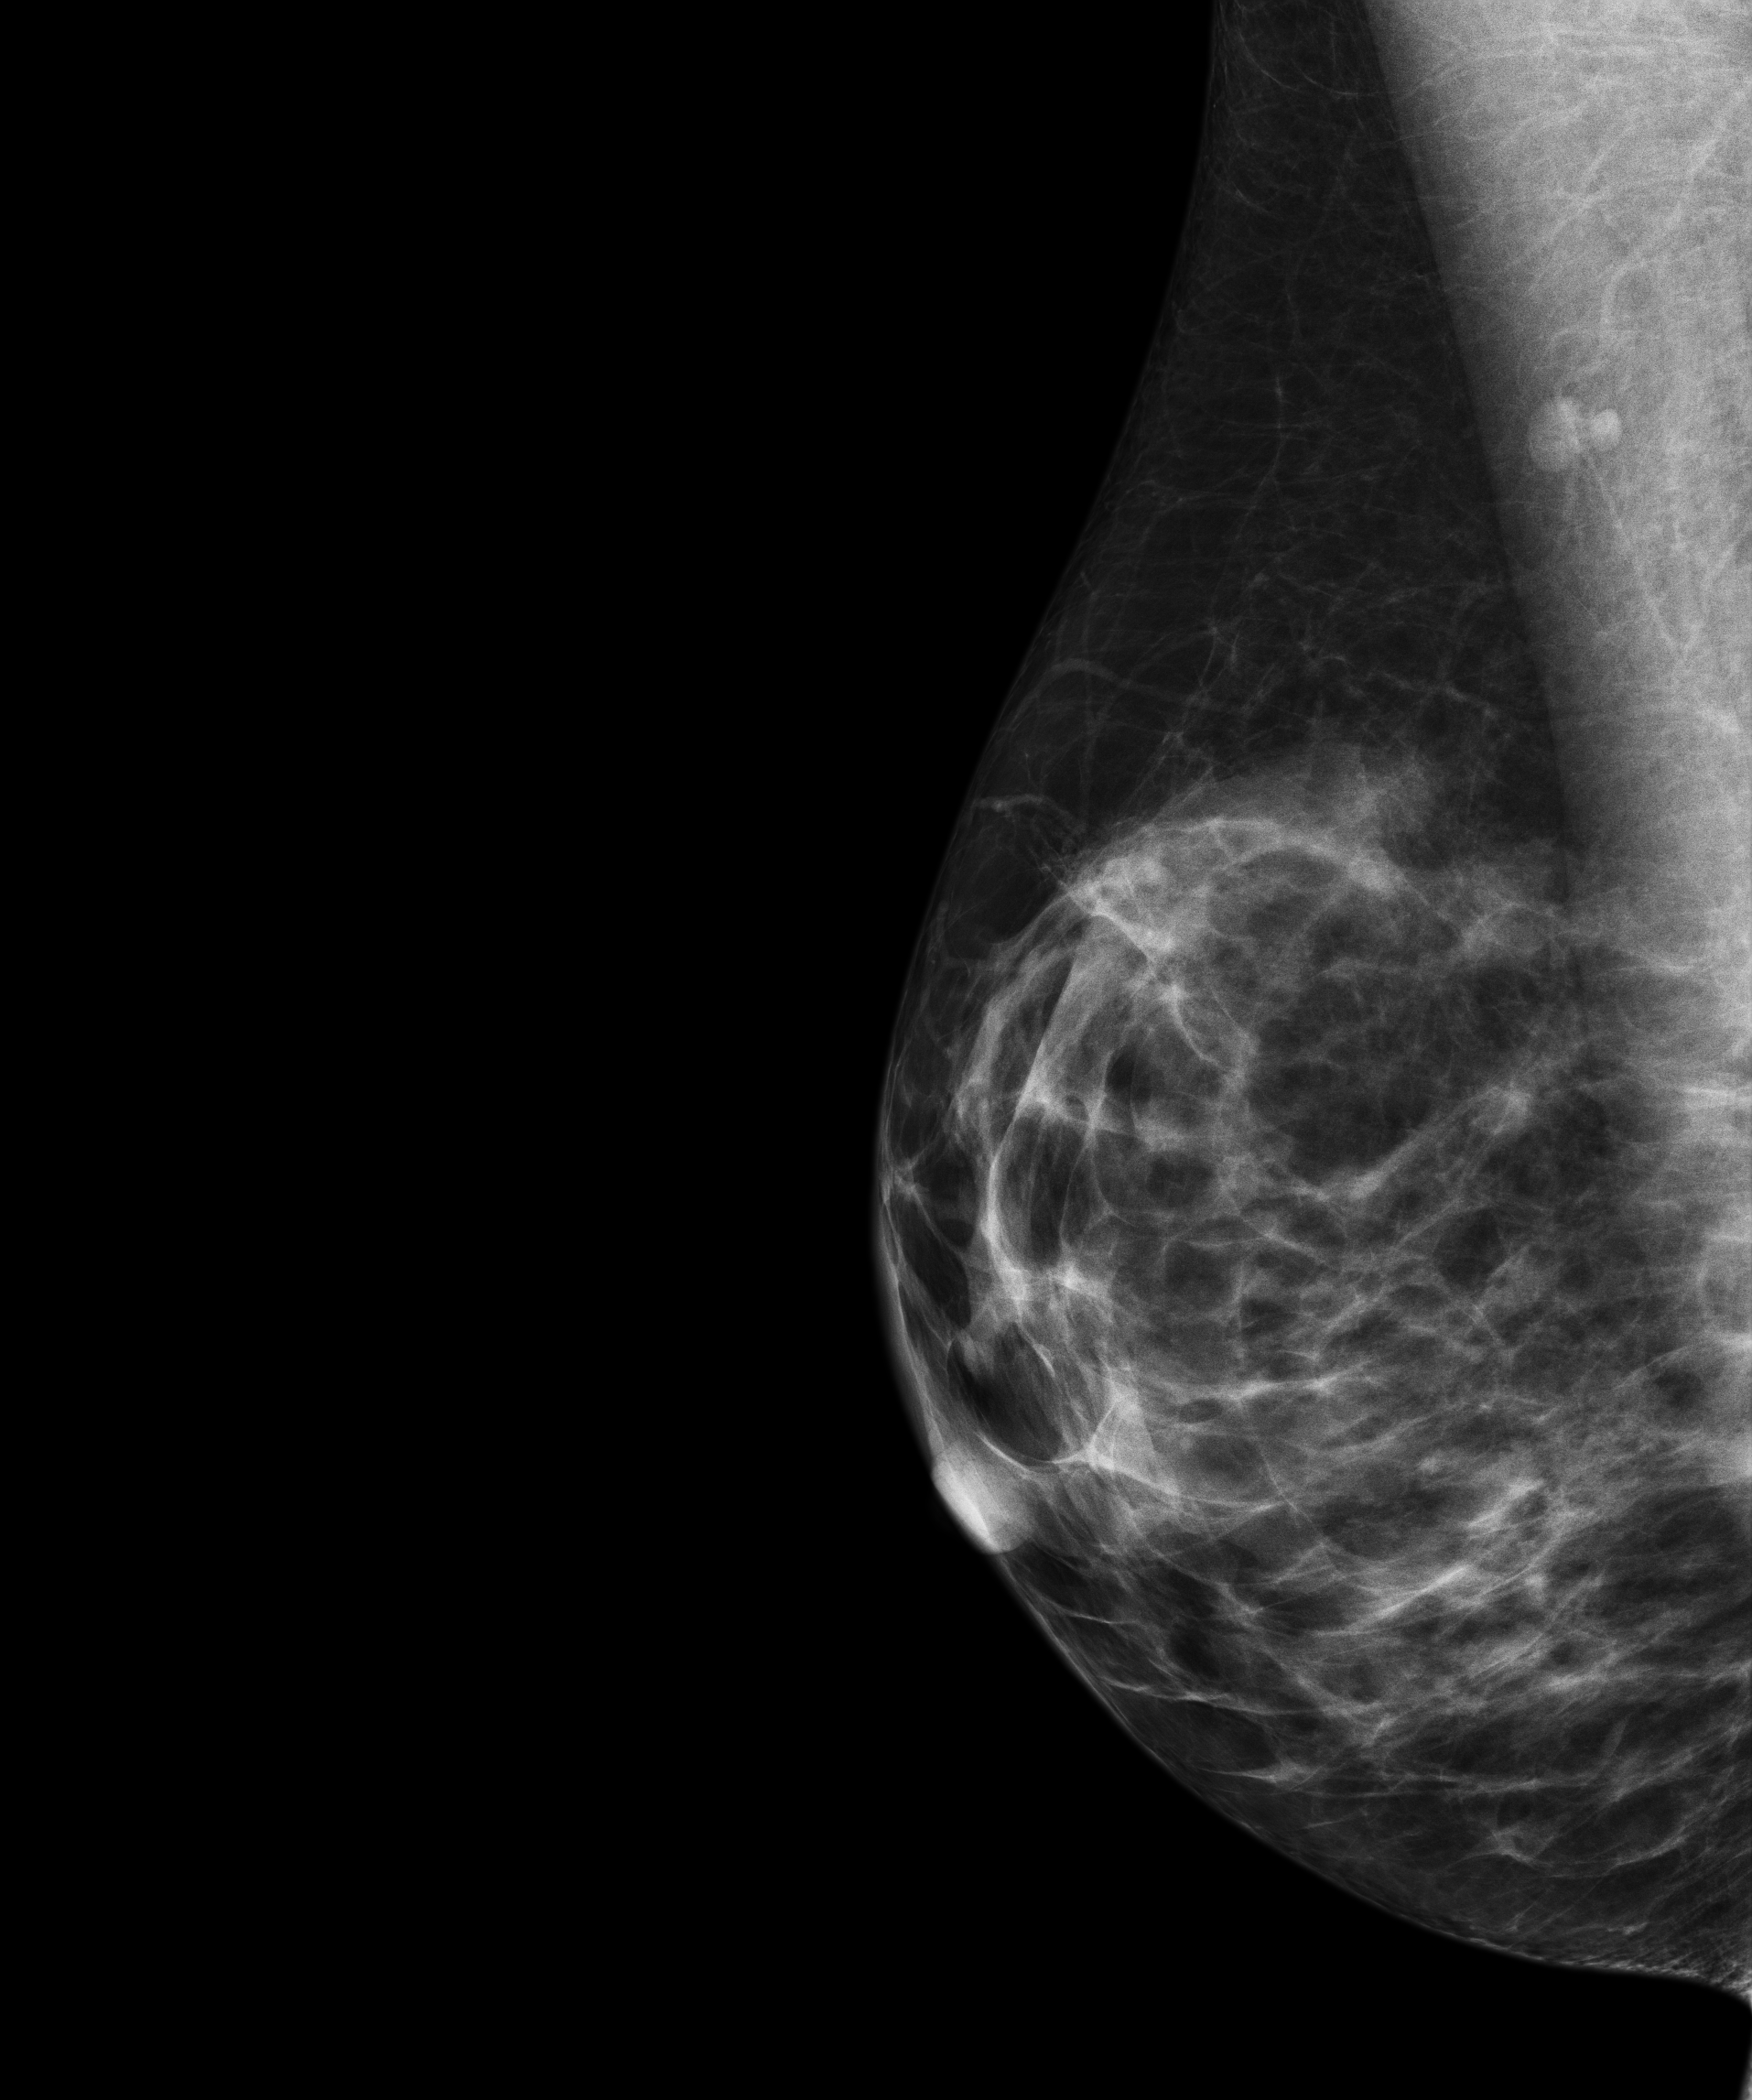
Full-field digital mammogram (FFDM), right breast, medio-lateral oblique projection, screening examination, compressed breast thickness 47 mm. Patient aged 45 years (female).
Final BI-RADS assessment for this screening round (tomosynthesis exam, both breasts): category 1.